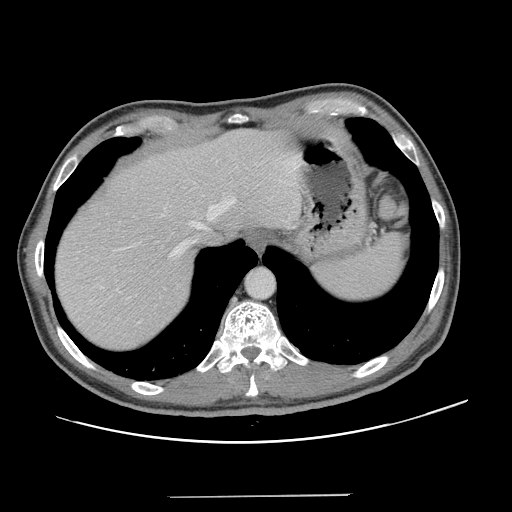
Contrast-enhanced abdominal CT, one axial slice. Position 110 of 131 along the scan axis. 120 kVp. Intravenous contrast given. Soft-tissue window (W 400 / L 40 HU). 512 × 512 image matrix. Male patient, age 60 years. From the clinical record (not read from this slice): diagnosis: colorectal cancer liver metastases, imaged before liver resection; multiple liver metastases: no; largest metastasis: 2.5 cm.
Annotated regions visible in this slice (expert manual segmentation):
- hepatic veins: box from (x=114, y=198) to (x=236, y=259) px
- liver: (x=56, y=129)–(x=301, y=352)
- planned liver remnant (the part of the liver to remain after resection): (x=56, y=129)–(x=301, y=343)